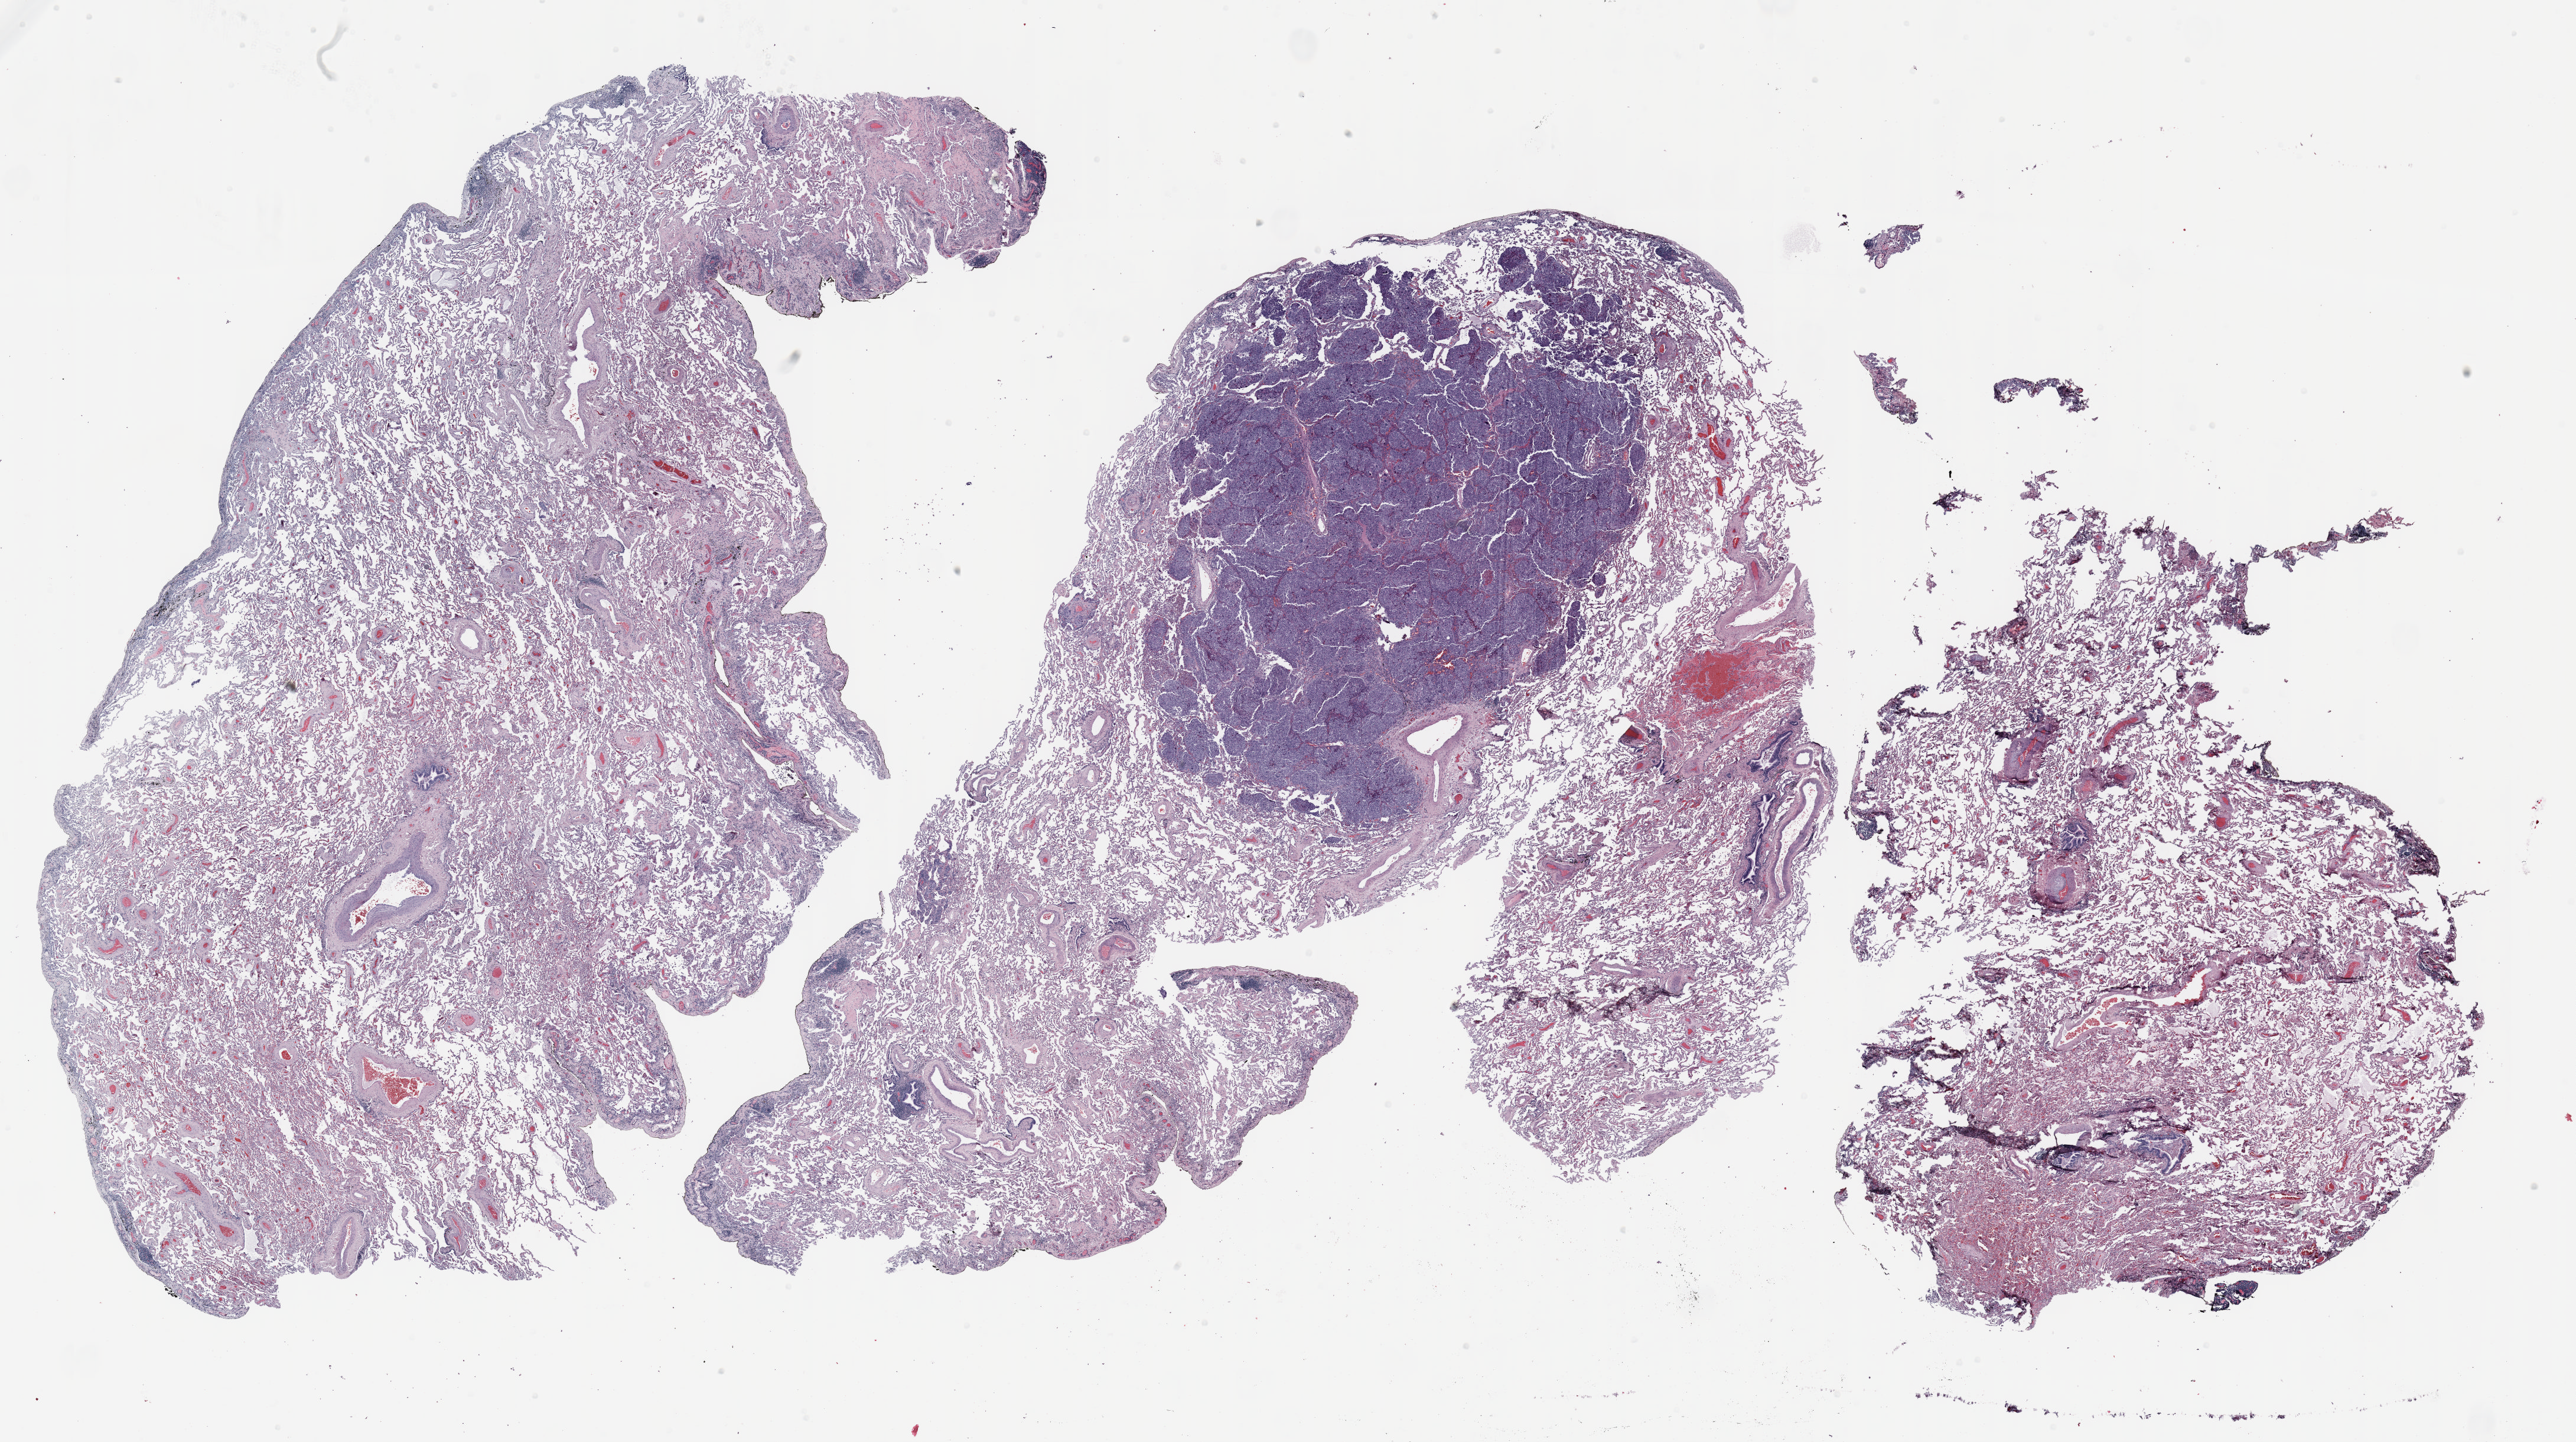
H&E whole-slide image — whole scanned area (about 35.0 x 19.6 mm, acquisition: 20x scan) shown as a low-resolution overview, formalin-fixed paraffin-embedded (FFPE) section, lung. Male, age 68 at enrolment. Current smoker at enrolment. Grade: poorly differentiated (G3).
- primary tumour location (clinical record): left upper lobe
- stage (AJCC 6th edition): IV
- participant's lung-cancer diagnosis: Non-small cell carcinoma
- tumour size (pathology): 30 mm